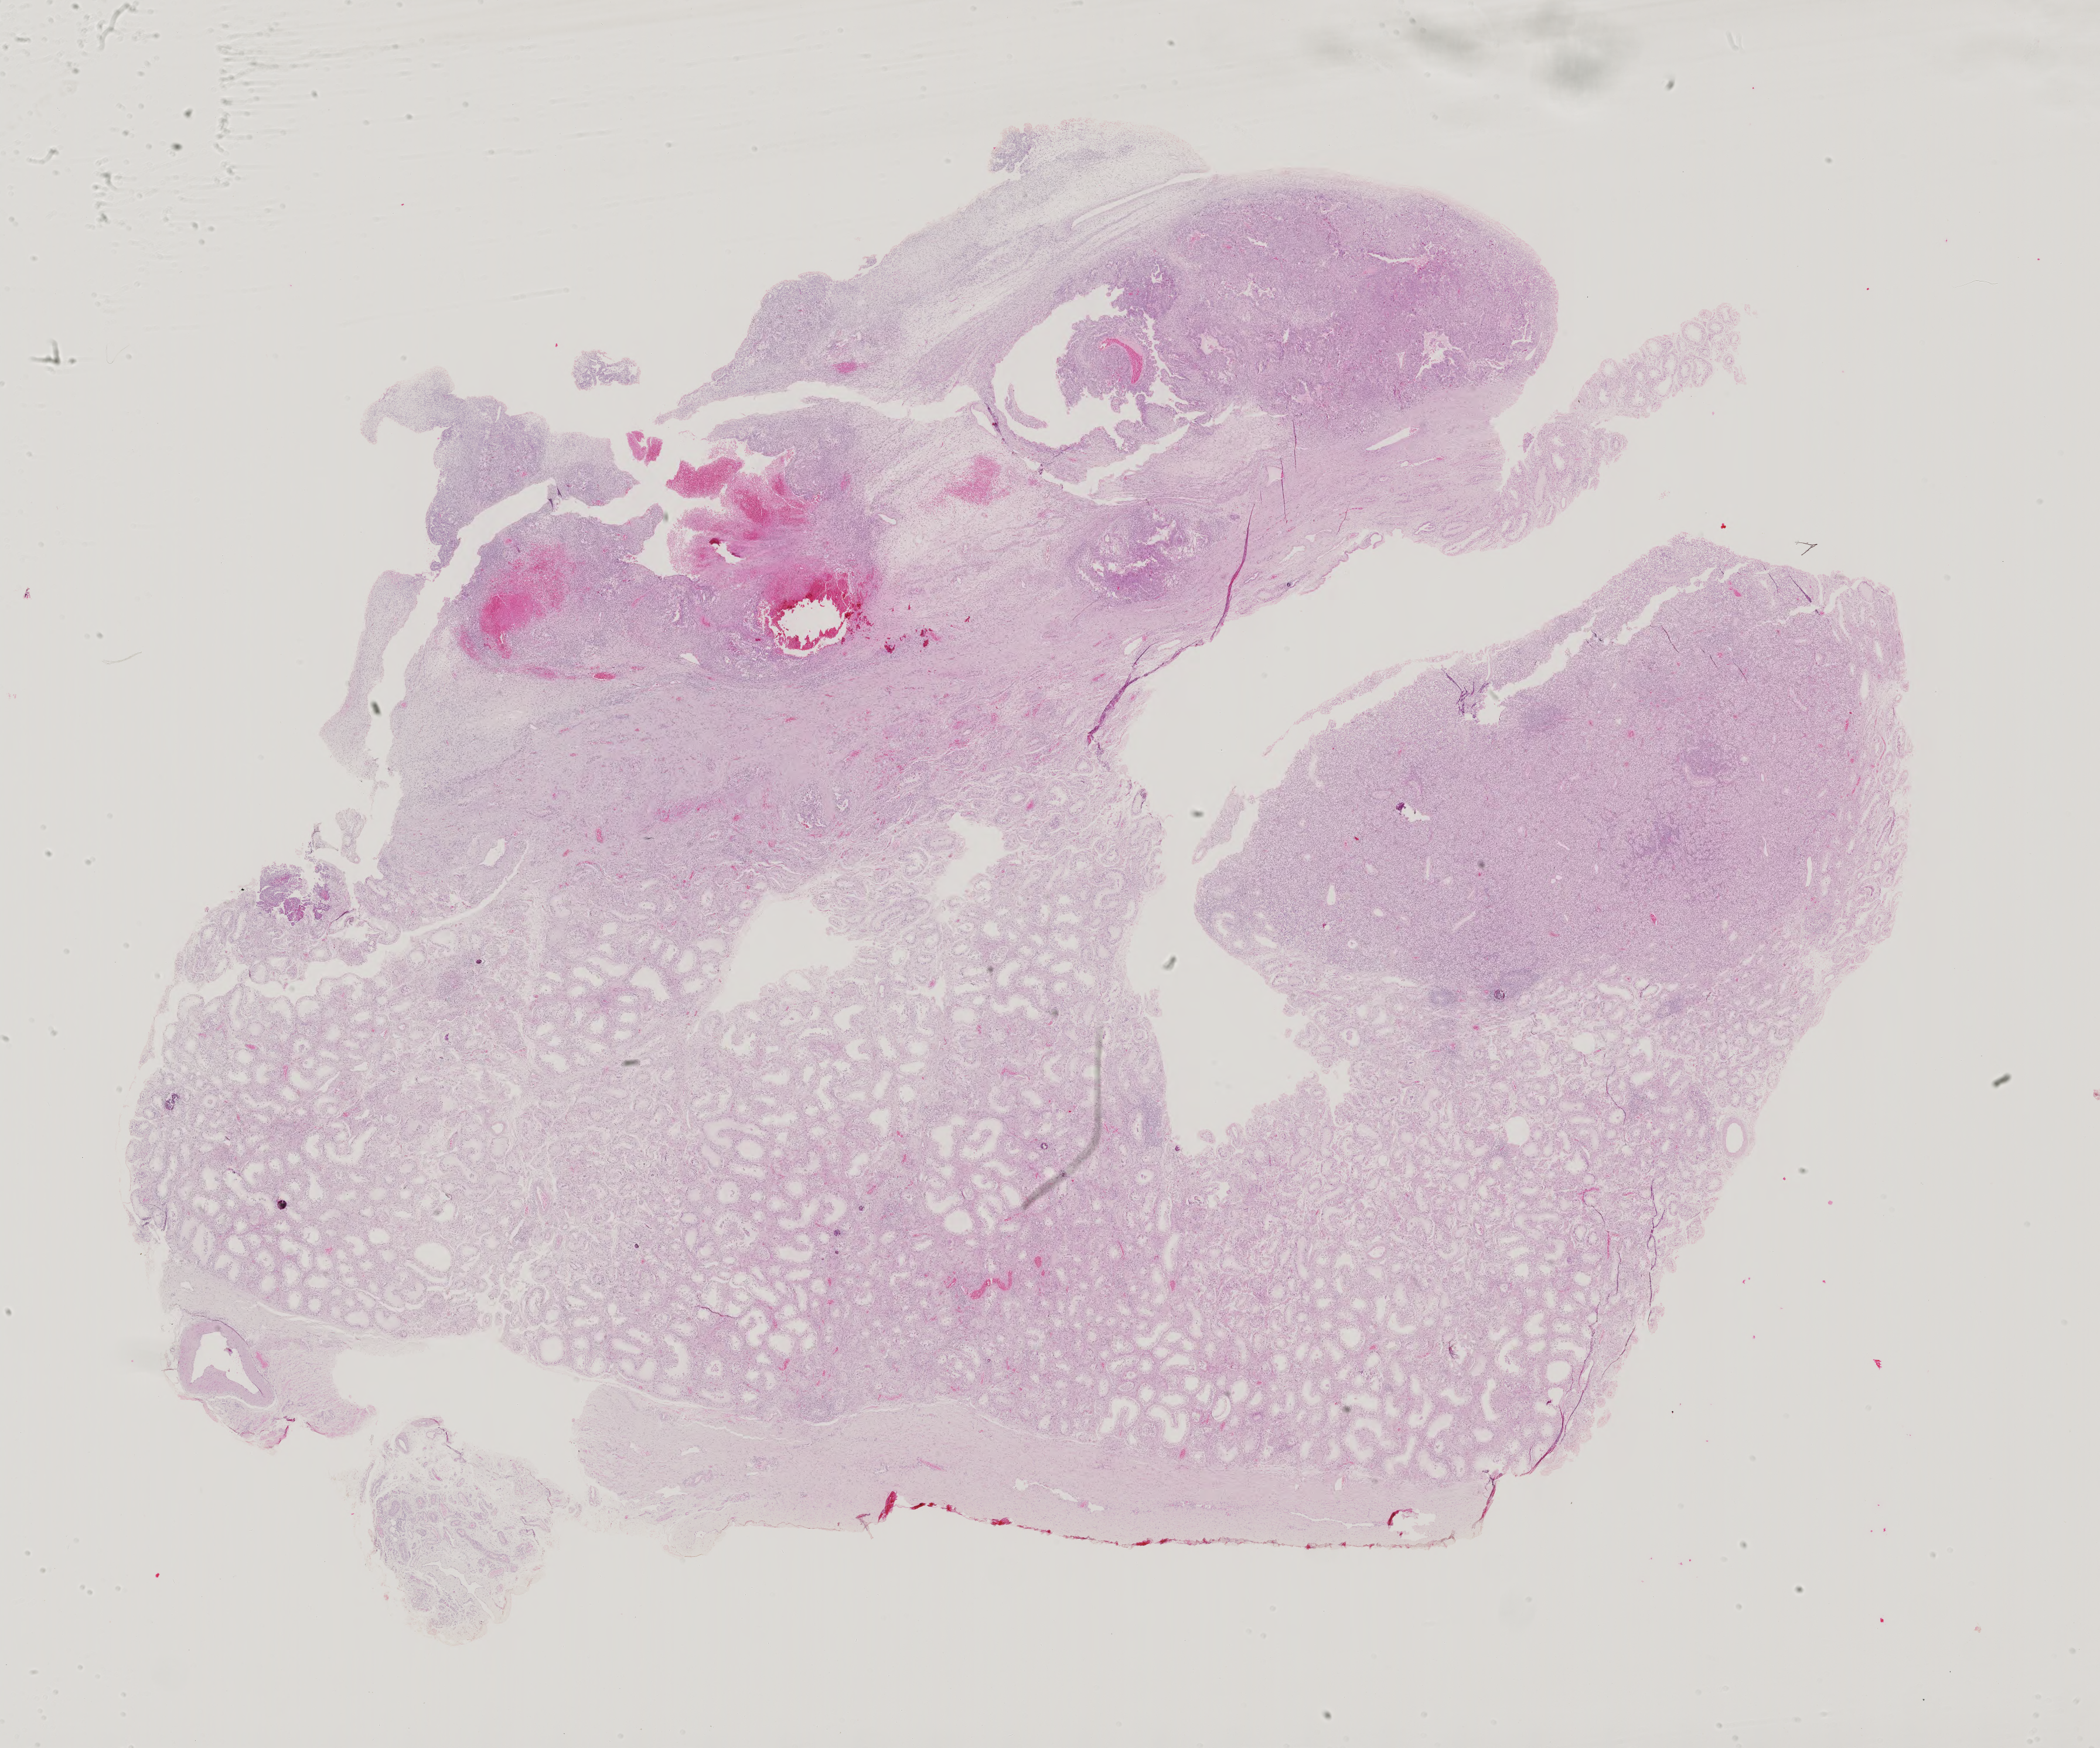
Hematoxylin and eosin (H&E) stained whole-slide image — whole scanned area (about 26.1 x 21.7 mm, acquisition: 40x scan) shown as a low-resolution overview. Patient sex: male.
Specimen: formalin-fixed paraffin-embedded (FFPE) diagnostic section; sample: primary tumour, testis.